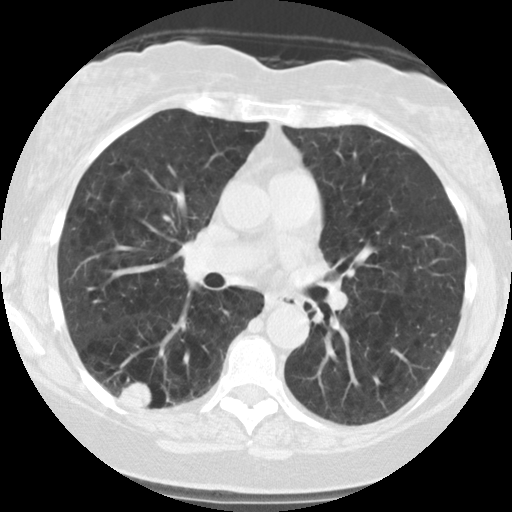
Low-dose screening chest CT, one axial slice; position 64 of 122 along the scan axis; reconstruction kernel STANDARD; 140 kVp; lung window (W 1500 / L -600 HU); 512 × 512 image matrix.
Annotated regions visible in this slice (expert manual segmentation):
- lesion 1 (tumor, lower lobe of right lung): bounding box <119,382,151,409> (left, top, right, bottom; pixels)